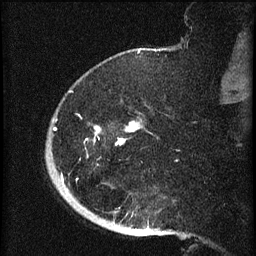
Breast MRI (dynamic contrast-enhanced), one sagittal slice. Position 14 of 60 along the scan axis. Dynamic contrast-enhanced series, image 2 of 3 at this slice position (ordered by acquisition). 1.5 T. TE 4.2 ms, TR 8.2 ms. 2 mm slice thickness. 256 × 256 image matrix. Patient: female, 71 years.
Annotated regions visible in this slice (semi-automatically segmented with operator editing):
- analysis volume of interest (the breast-tissue region the enhancement analysis was run in; not a lesion): box from (x=46, y=73) to (x=147, y=196) px
- tumour enhancement mask (voxels above the 70 % enhancement threshold inside the analysis volume of interest): (x=53, y=122)–(x=139, y=183)